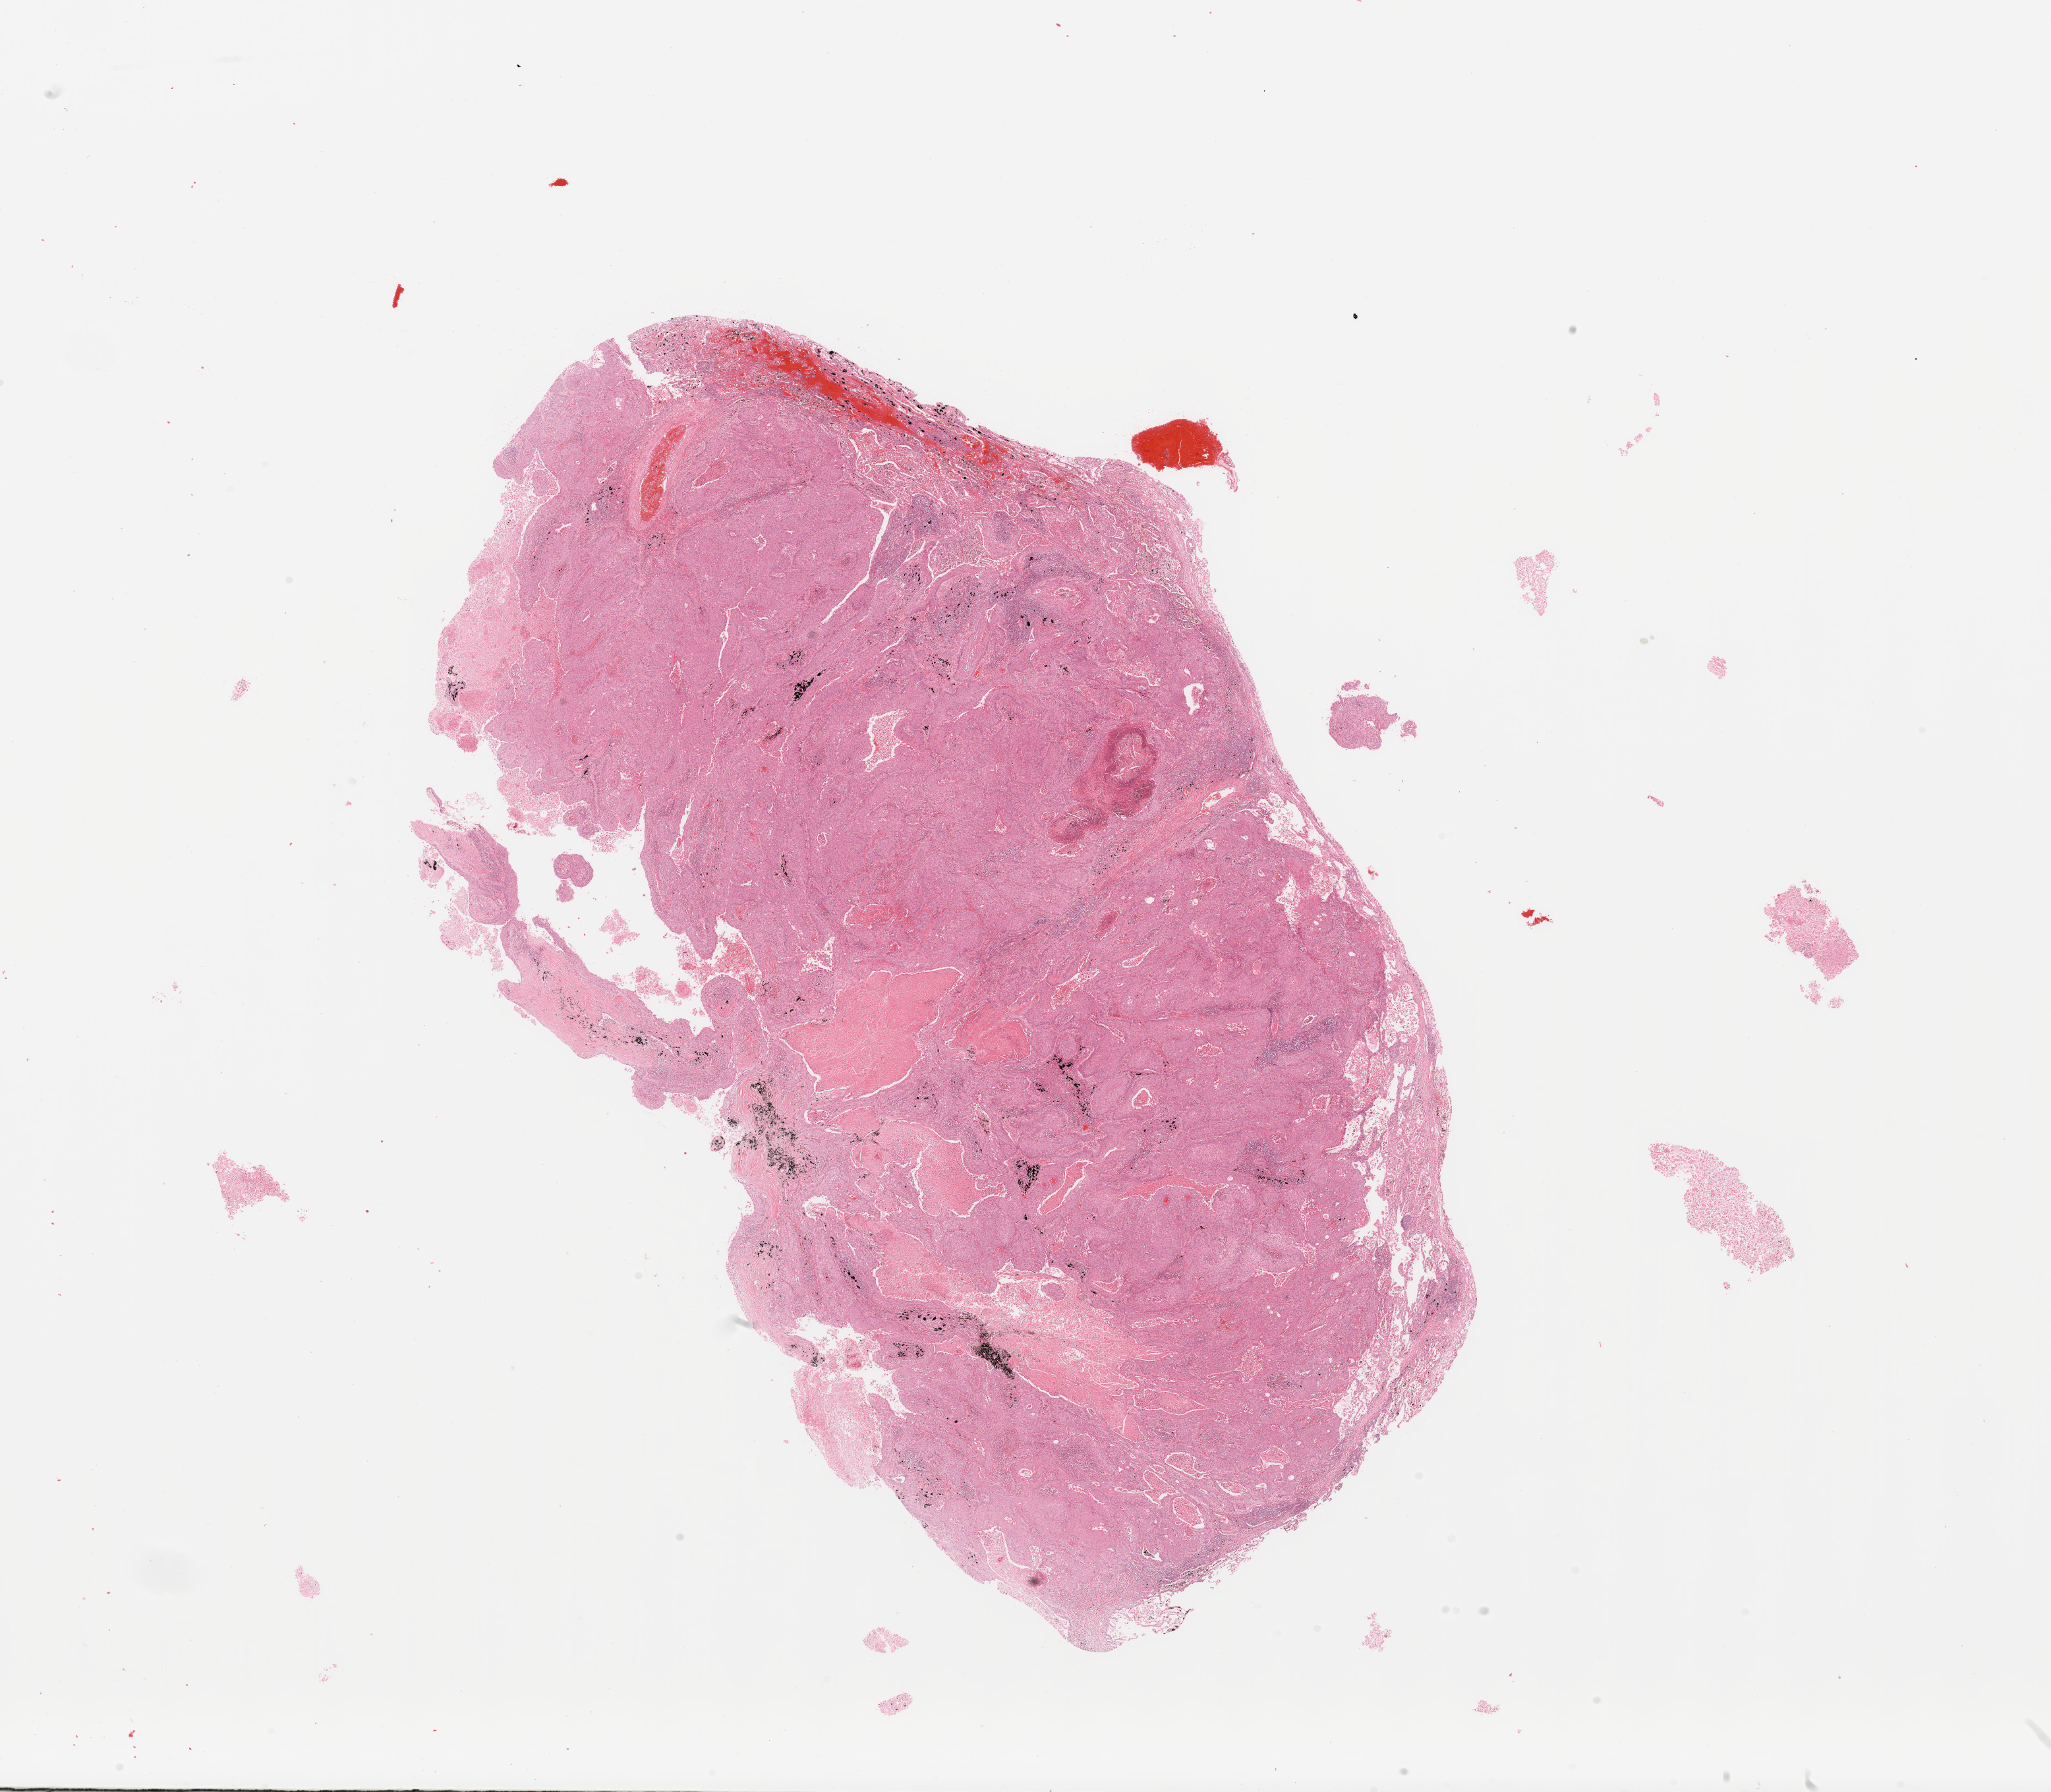
Whole-slide histology image, H&E-stained, low-resolution overview of the scanned area, about 24.6 x 21.5 mm; tumour tissue sample, sampled site: lung. 56-year-old male patient. Histologic grade: G2 (moderately differentiated). Slide review estimates, as recorded: tumour nuclei 70%, necrosis 15%.
AJCC pathologic stage: IIB. Diagnosis: Squamous cell carcinoma, NOS.